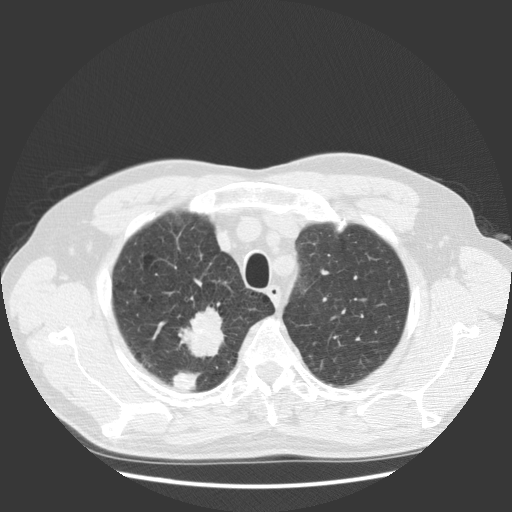
Low-dose screening chest CT, one axial slice; slice 105 of 131 in the series (ordered by position); reconstruction kernel STANDARD; lung window (W 1500 / L -600 HU); 2.5 mm slice thickness; 512 × 512 image matrix.
Annotated regions visible in this slice (expert manual segmentation):
- lesion 1 (tumor, upper lobe of right lung): bounding box (x1, y1, x2, y2) in pixels: (178, 306, 225, 358)
- lesion 2 (tumor, upper lobe of right lung): (172, 372, 200, 392)